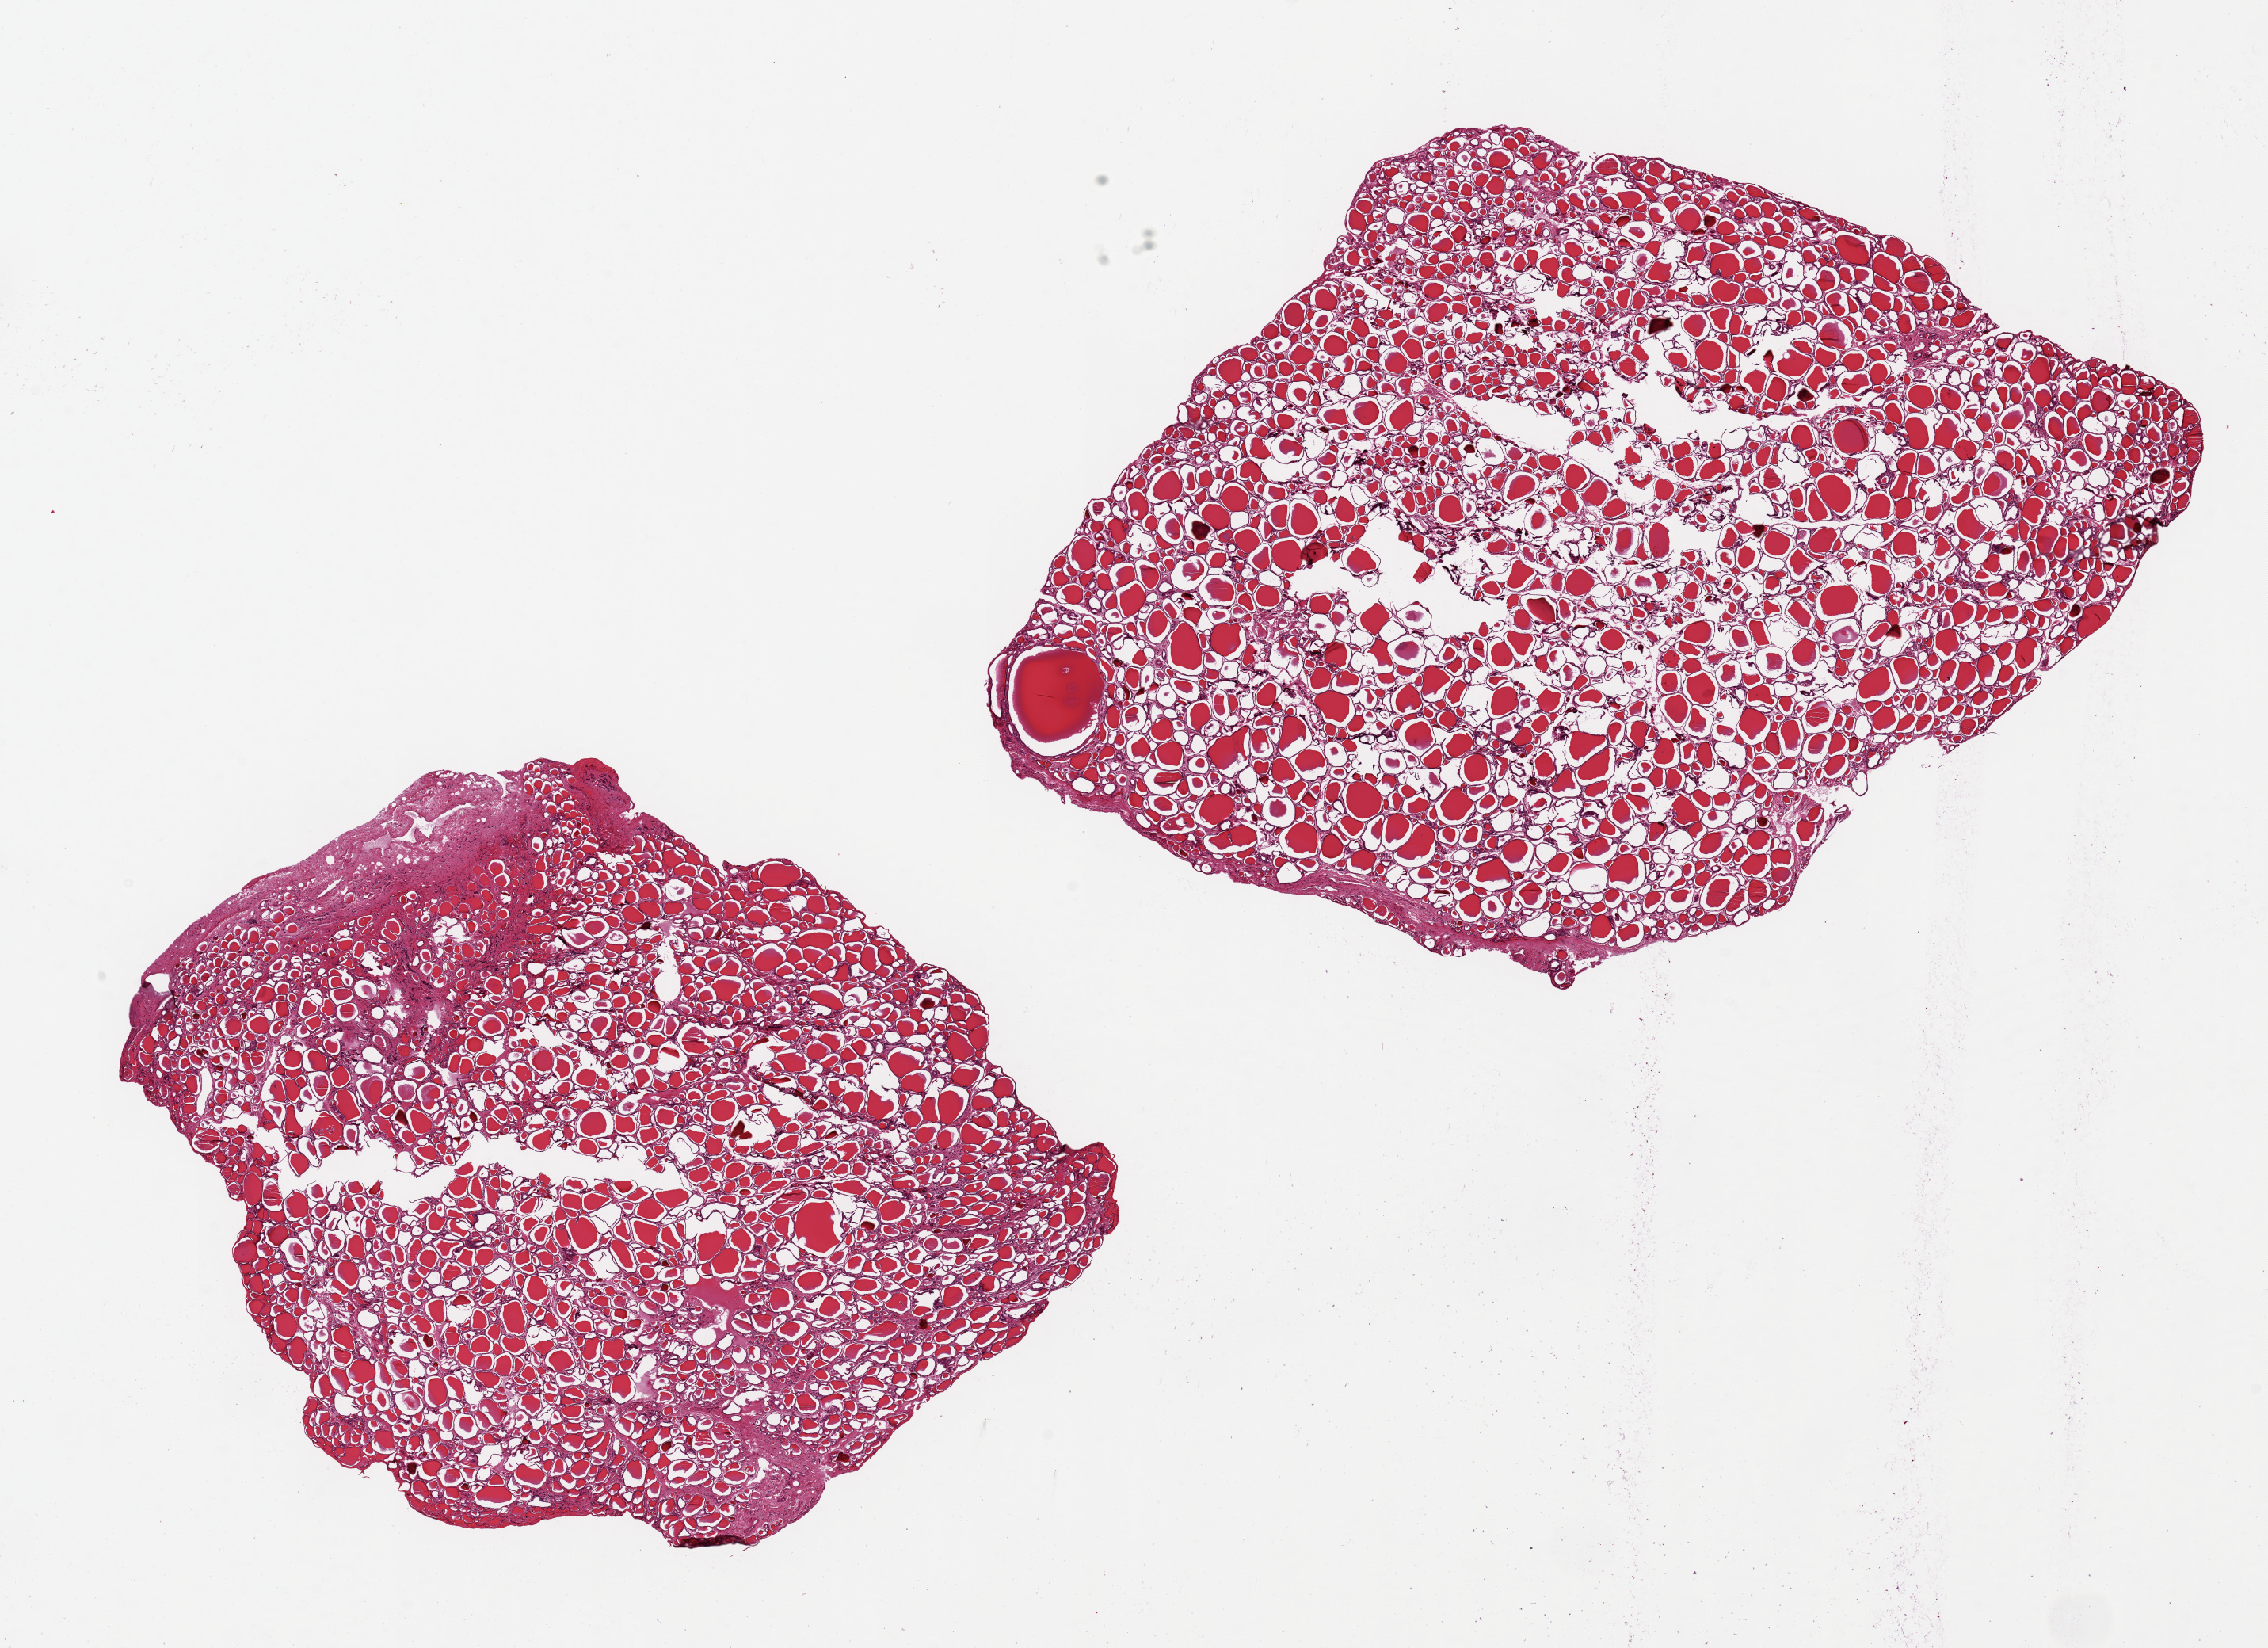
Hematoxylin and eosin (H&E) whole-slide image — shown as a low-resolution overview of the whole scanned area (about 22.6 x 16.4 mm); PAXgene-fixed paraffin-embedded (PFPE) section; section of thyroid (target tissue); tissue donor sample. Donor sex: female.
Pathologist's review note for this sample: 2 pieces 7x6 & 9x7 mm; uniform structure.